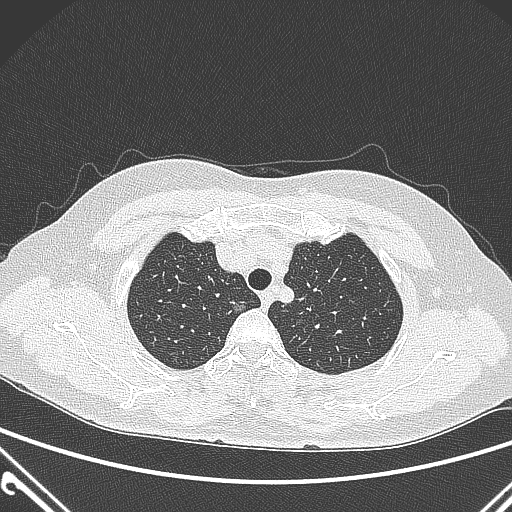
Chest CT, one axial slice; slice 235 of 300 in the series (ordered by position); 120 kVp; lung window (W 1500 / L -600 HU); 1 mm slice thickness; 512 × 512 image matrix, field of view 350 × 350 mm. Patient: female, 54 years. Case-level facts recorded for this patient, not image findings: clinical TNM (as recorded): T1a N0 M0.
Outlined on this slice (bounding box drawn by a radiologist):
- lung tumour (recorded histology: adenocarcinoma): bounding box [x1, y1, x2, y2] px = [219, 291, 253, 324]